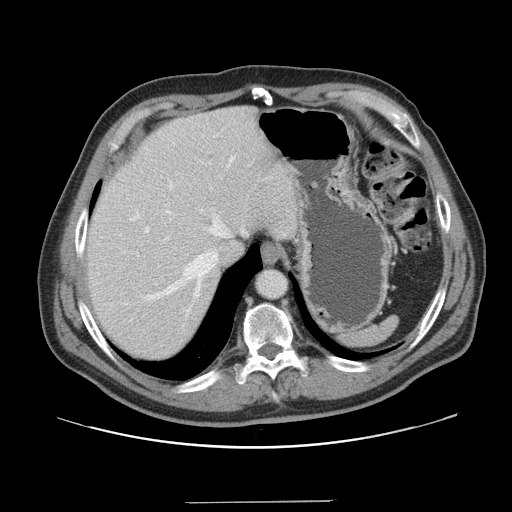
Contrast-enhanced abdominal CT, one axial slice; position 127 of 151 along the scan axis; 120 kVp; soft-tissue window (W 400 / L 40 HU); 512 × 512 image matrix, field of view 399 × 399 mm. Male patient, age 63 years. From the clinical record (not read from this slice): diagnosis: colorectal cancer liver metastases, imaged before liver resection.
Structures marked on this image (outlined manually by an expert reader):
- hepatic veins: bounding box <130,157,244,299> (left, top, right, bottom; pixels)
- liver: <86,107,300,361>
- planned liver remnant (the part of the liver to remain after resection): <86,120,253,361>